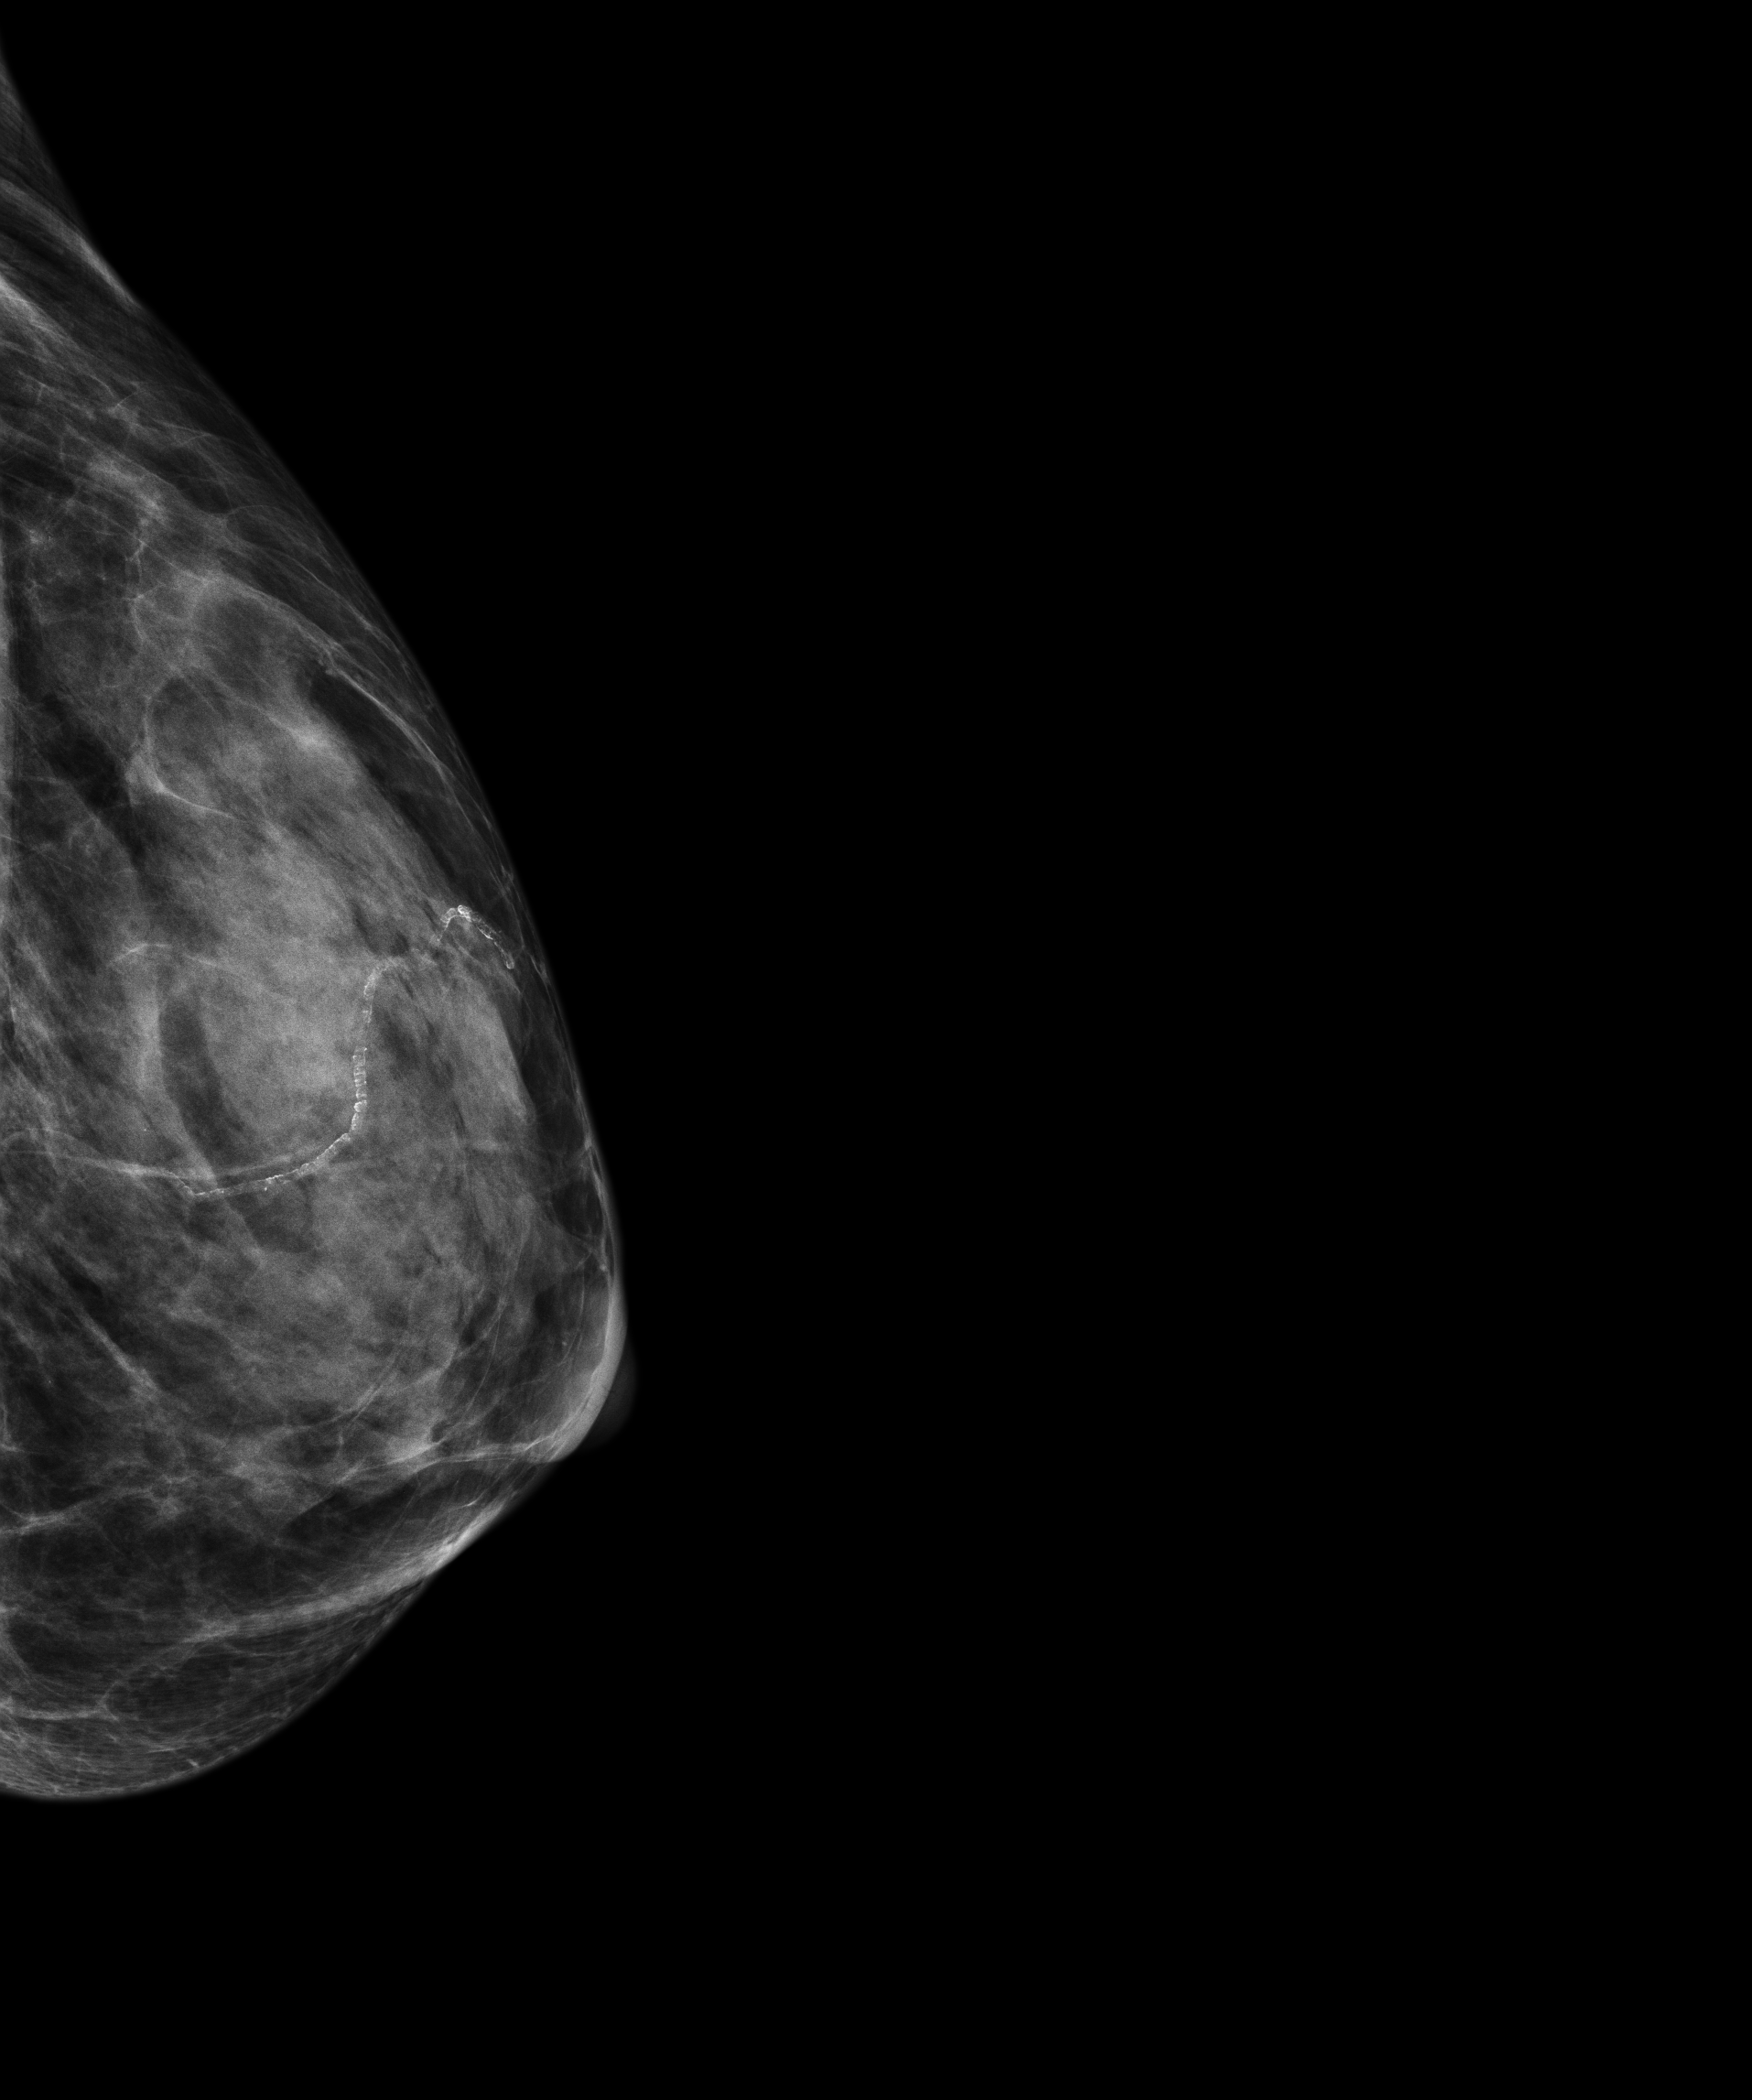
Screening examination, system: Senographe Essential ADS_56.21.3. Patient: female, 60 years.
Image type: full-field digital mammogram. Breast: left. Projection: exaggerated CC view (lateral).